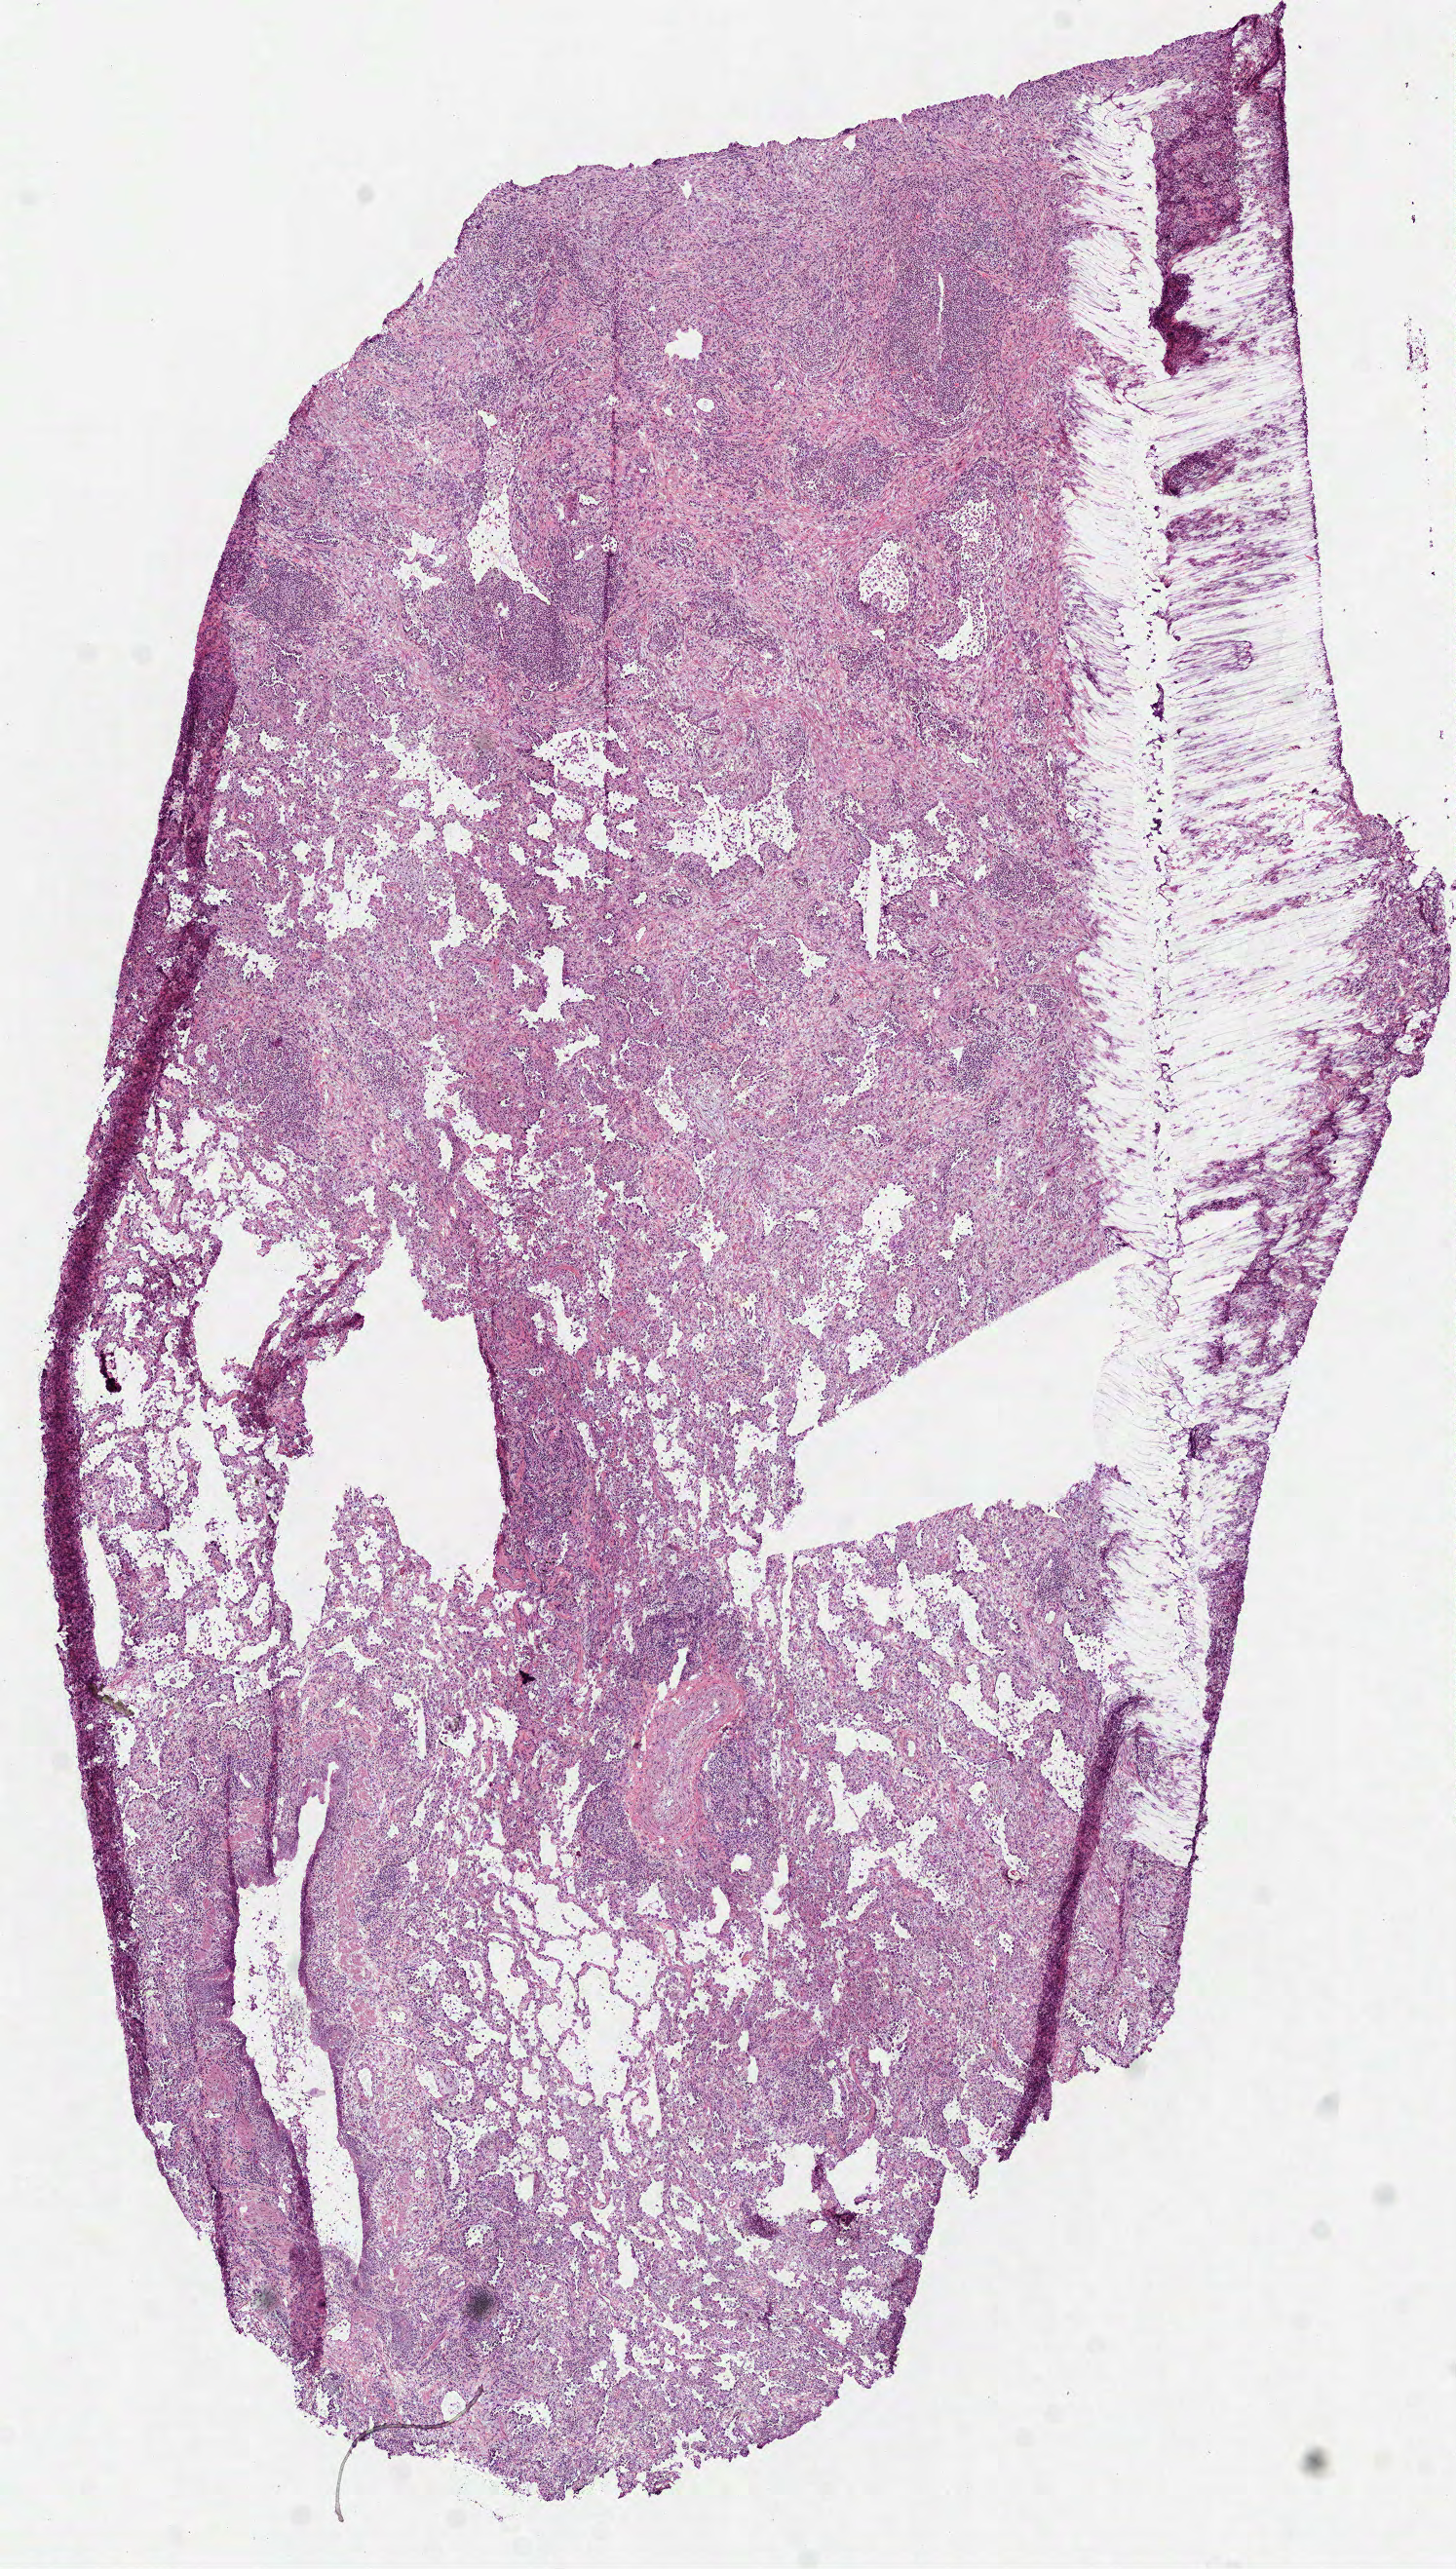
H&E-stained whole-slide image, whole scanned area (about 6.0 x 10.6 mm, slide scanned at 40x) shown as a low-resolution overview, frozen section from the bottom of the tissue portion, sample: primary tumour, lung. Female patient; age at initial diagnosis 69 years. Slide review estimates, as recorded: tumour cells 10%, tumour nuclei 10%, normal cells 90%, stromal cells 0%, necrosis 0%. Inflammatory infiltration, as recorded: lymphocyte infiltration 50%, monocyte infiltration 2%, neutrophil infiltration 10%.
Pathologic diagnosis: Squamous cell carcinoma, NOS. Laterality: right. AJCC pathologic stage: IIB (7th edition). TNM: T2b N1 MX.